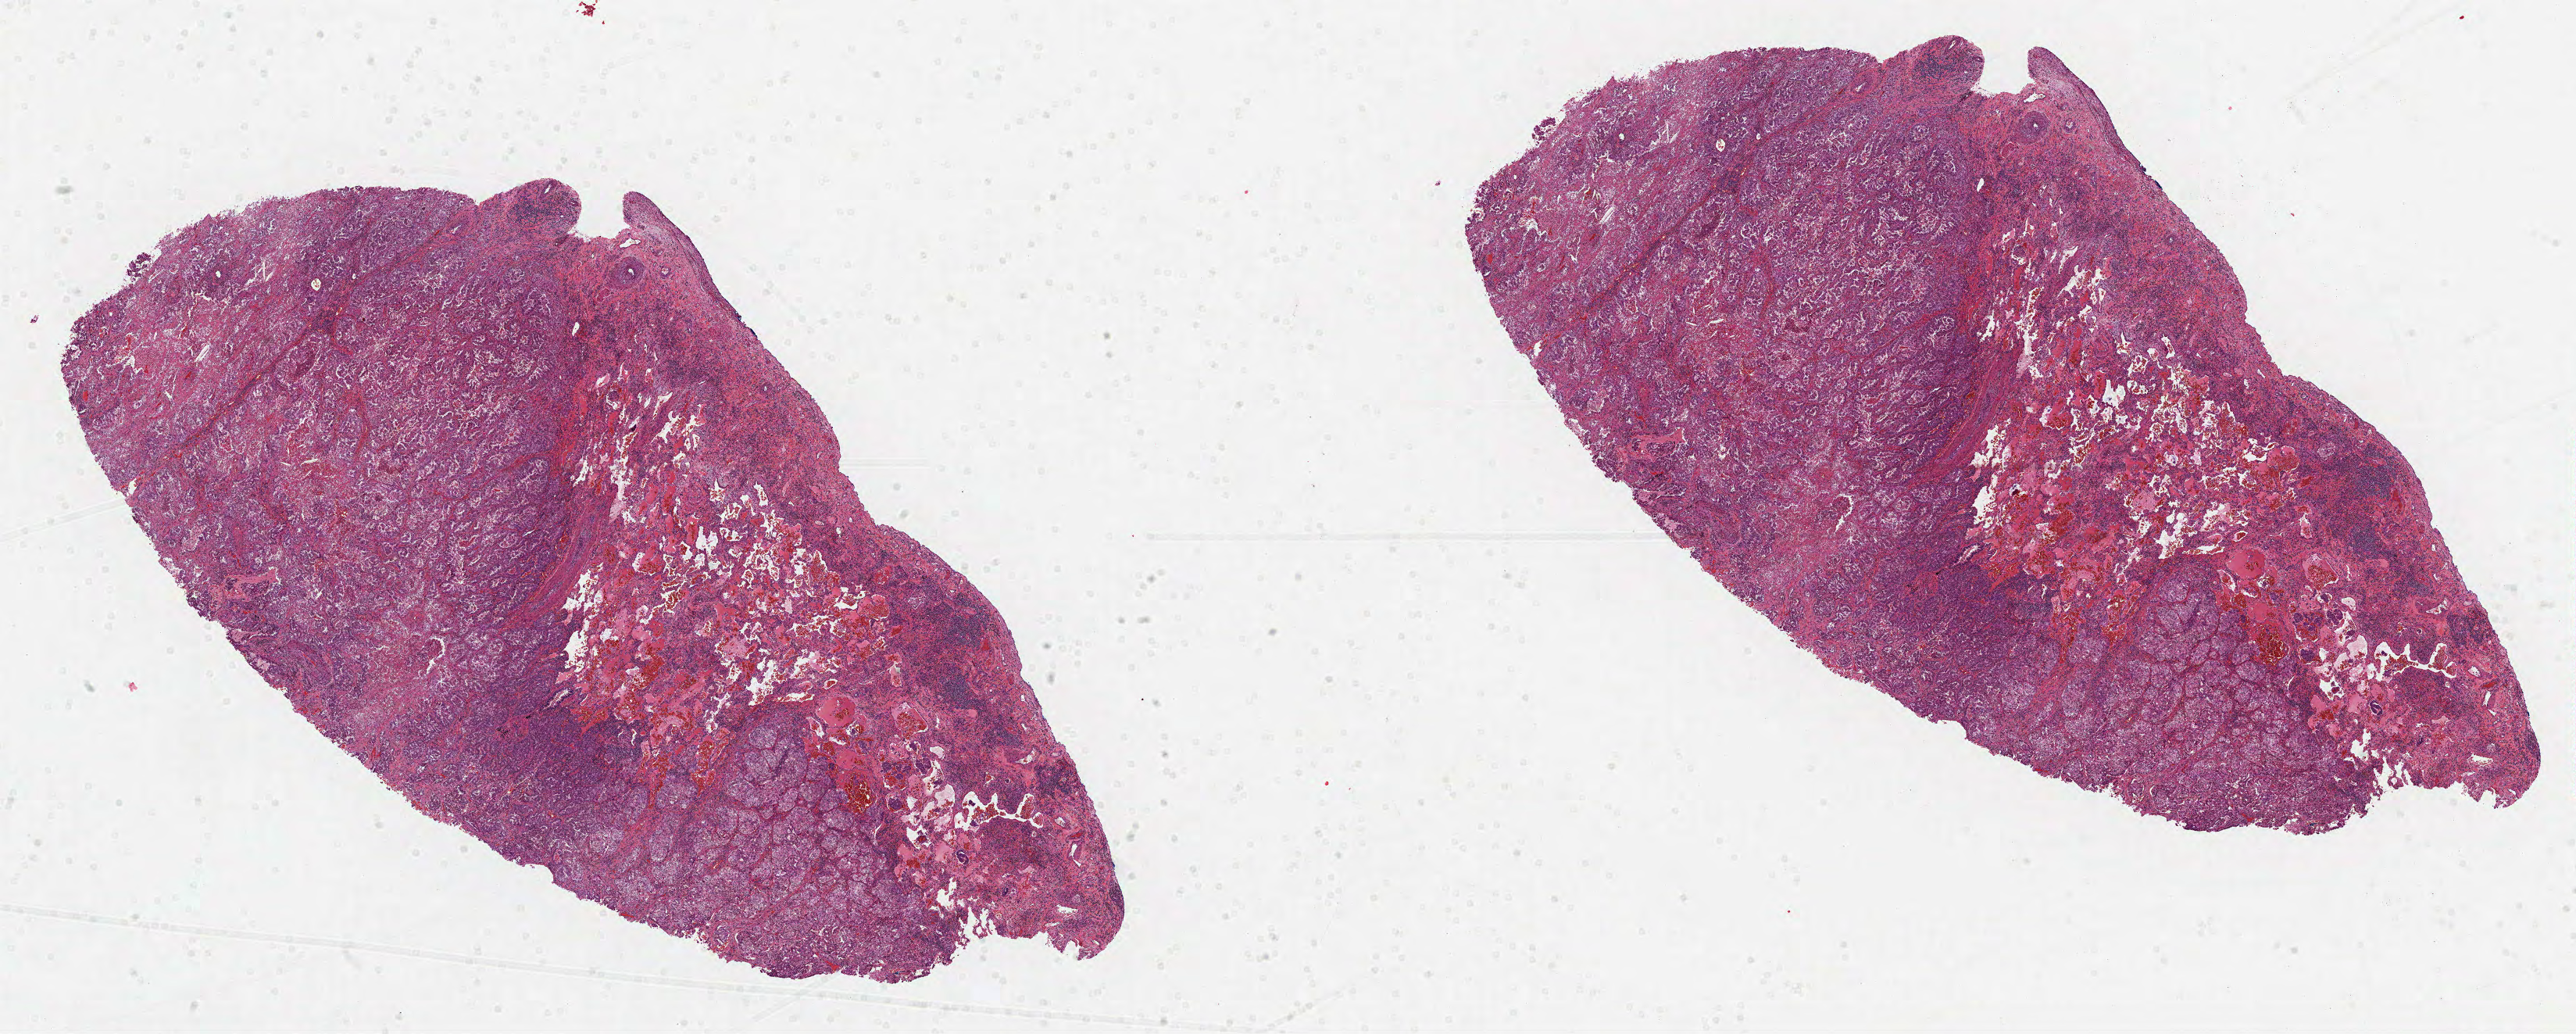
H&E whole-slide image, low-resolution overview of the scanned area, about 26.6 x 10.7 mm (acquisition: 40x scan). Formalin-fixed paraffin-embedded (FFPE) diagnostic section. Lung, primary tumour sample. Patient: female, age at initial diagnosis 60 years.
TNM: T2a N0 M0. AJCC pathologic stage: IB (6th edition). Diagnosis: Adenocarcinoma, NOS.